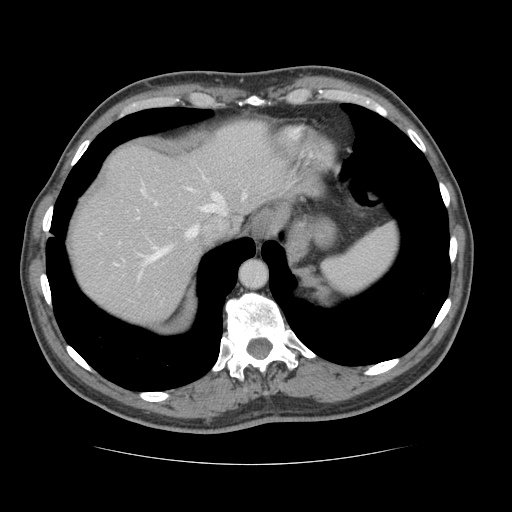
Contrast-enhanced abdominal CT, one axial slice. Position 110 of 134 along the scan axis. Reconstruction kernel STANDARD. 120 kVp. Intravenous contrast given. Soft-tissue window (W 400 / L 40 HU). 2.5 mm slice thickness. 512 × 512 image matrix, field of view 377 × 377 mm. Male patient, age 68 years. From the clinical record (not read from this slice): diagnosis: colorectal cancer liver metastases, imaged before liver resection; multiple liver metastases: yes; largest metastasis: 2.2 cm; disease in both lobes: no.
Structures marked on this image (manually delineated by an expert):
- hepatic veins: bounding box <116,186,247,278> (left, top, right, bottom; pixels)
- liver: <71,122,287,320>
- planned liver remnant (the part of the liver to remain after resection): <71,121,286,309>